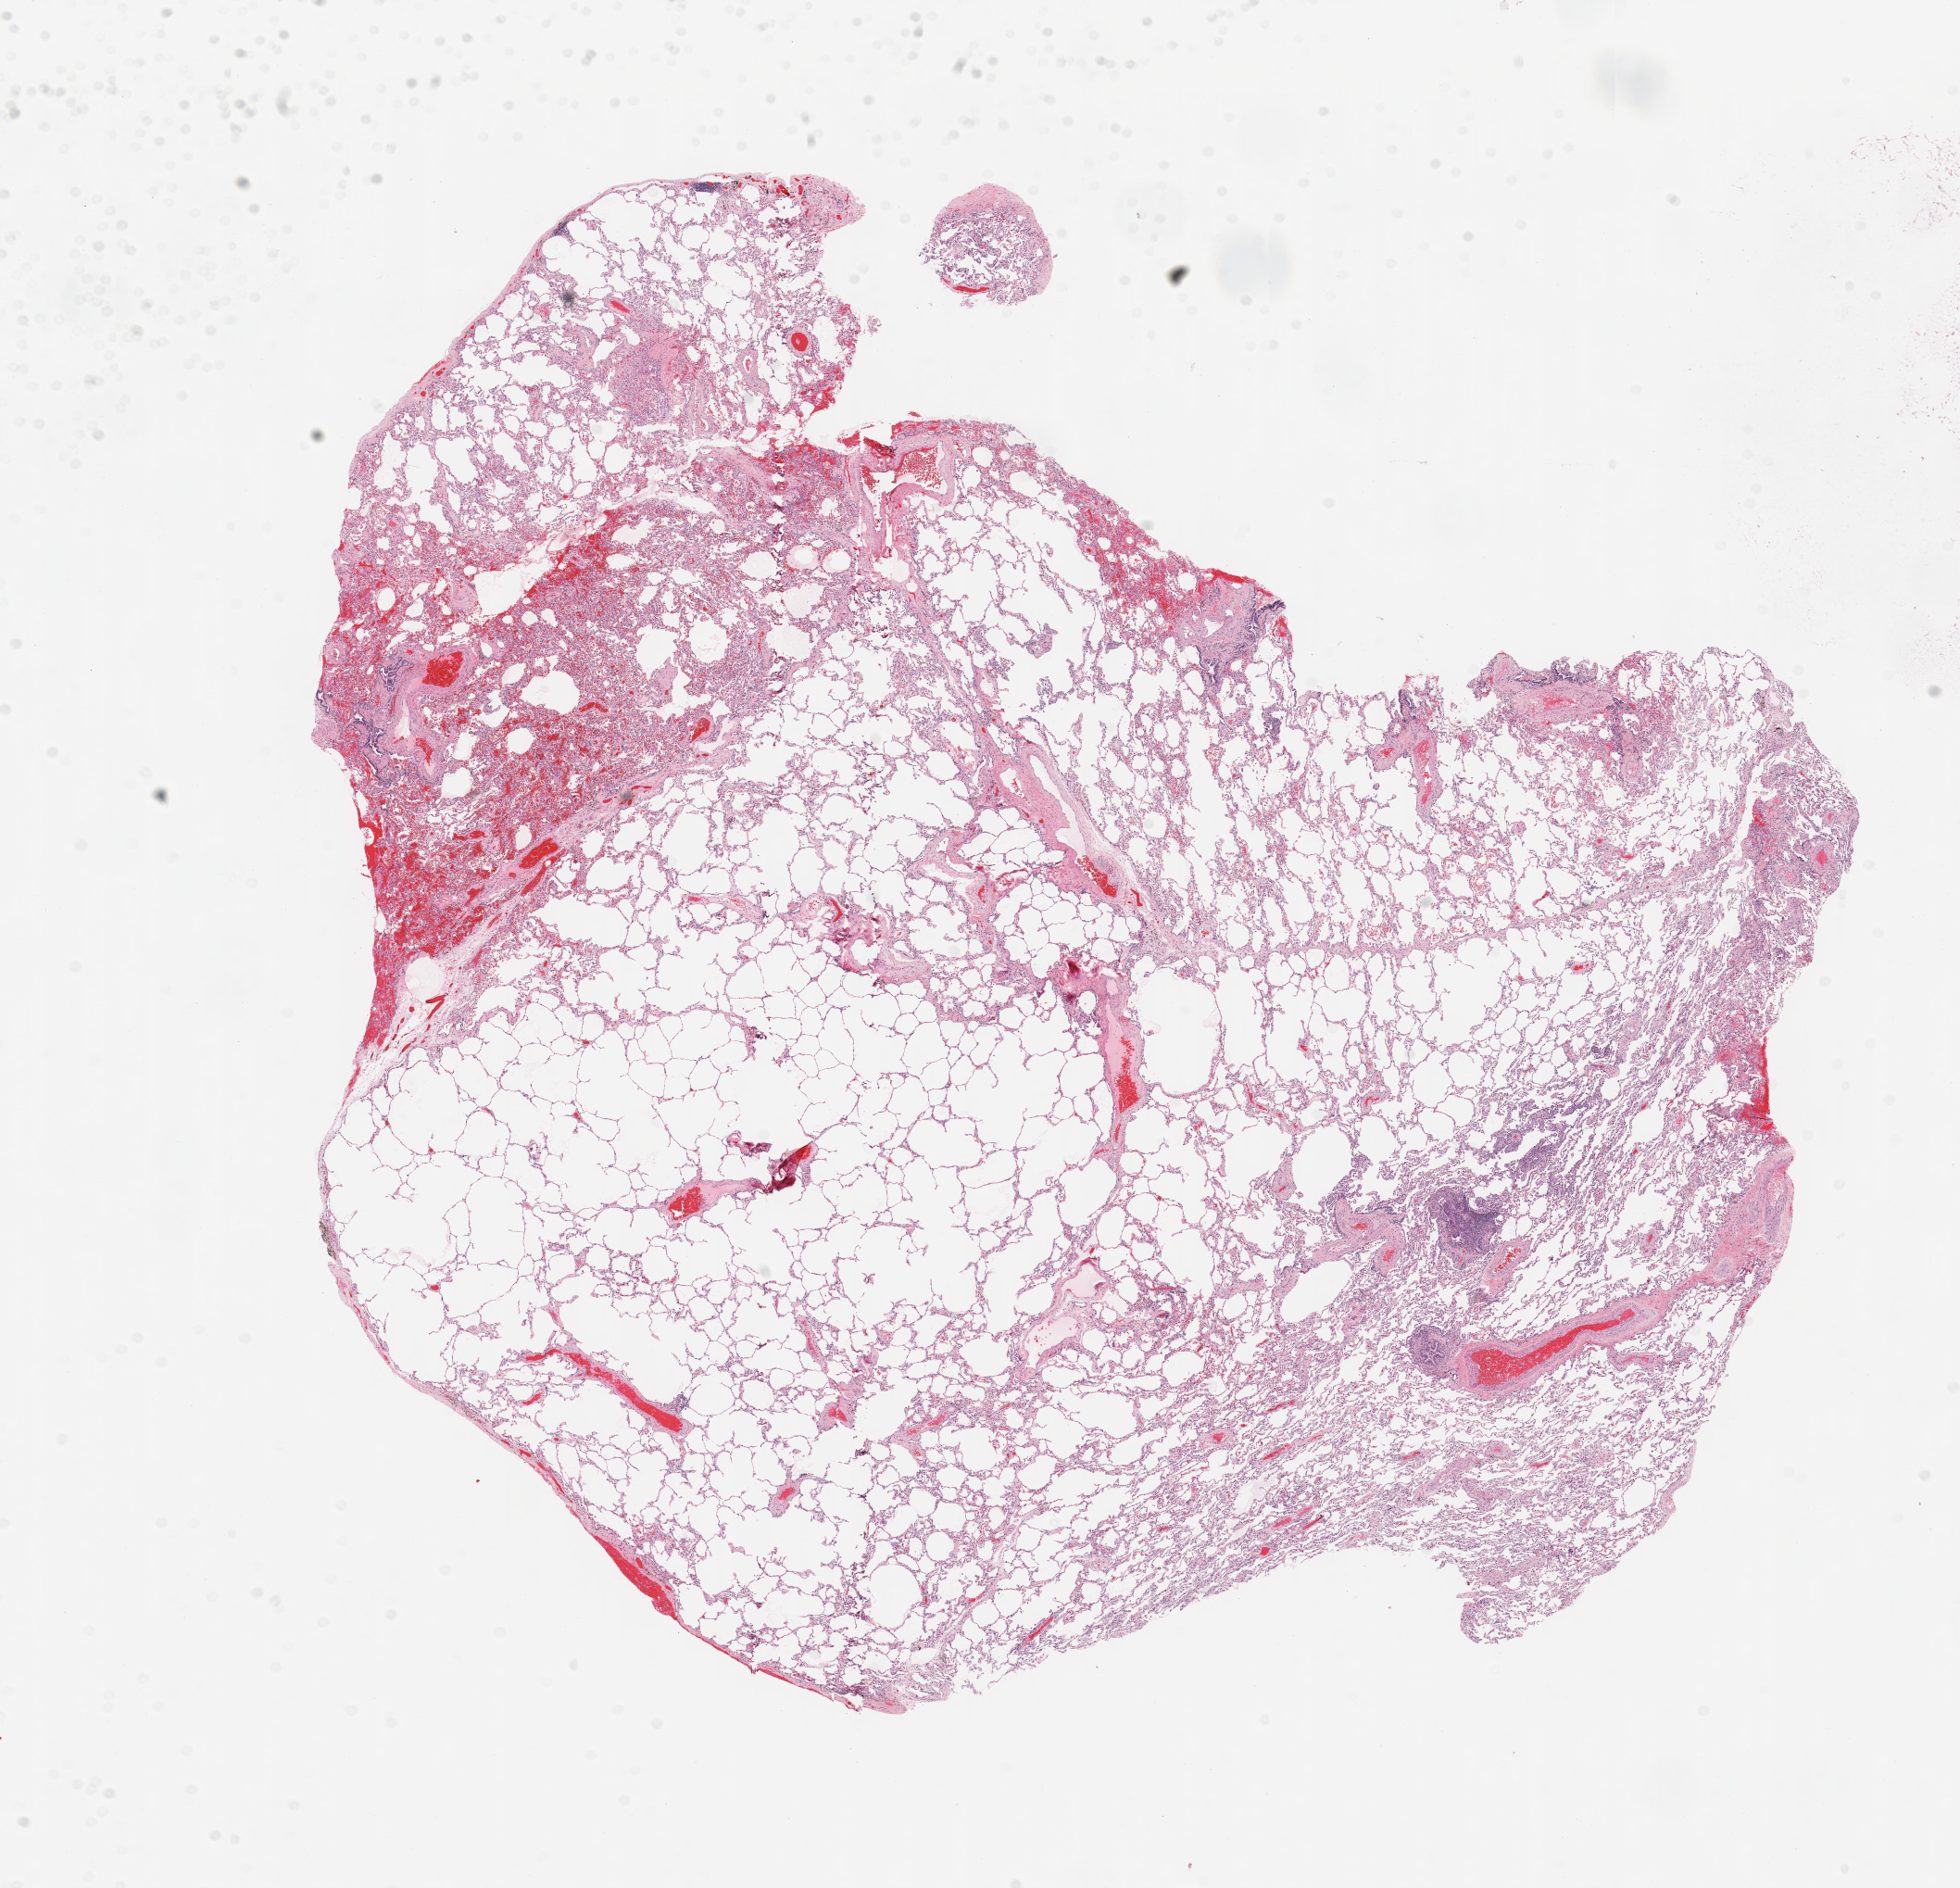
Whole-slide histology image, H&E, shown as a low-resolution overview of the whole scanned area (about 16.7 x 16.1 mm, from a 20x scan). Normal (non-tumour) tissue sample, sampled site: lung. Male, 69 y/o.
This section: normal (non-tumour) tissue from the same patient. Patient diagnosis: Adenocarcinoma, NOS.